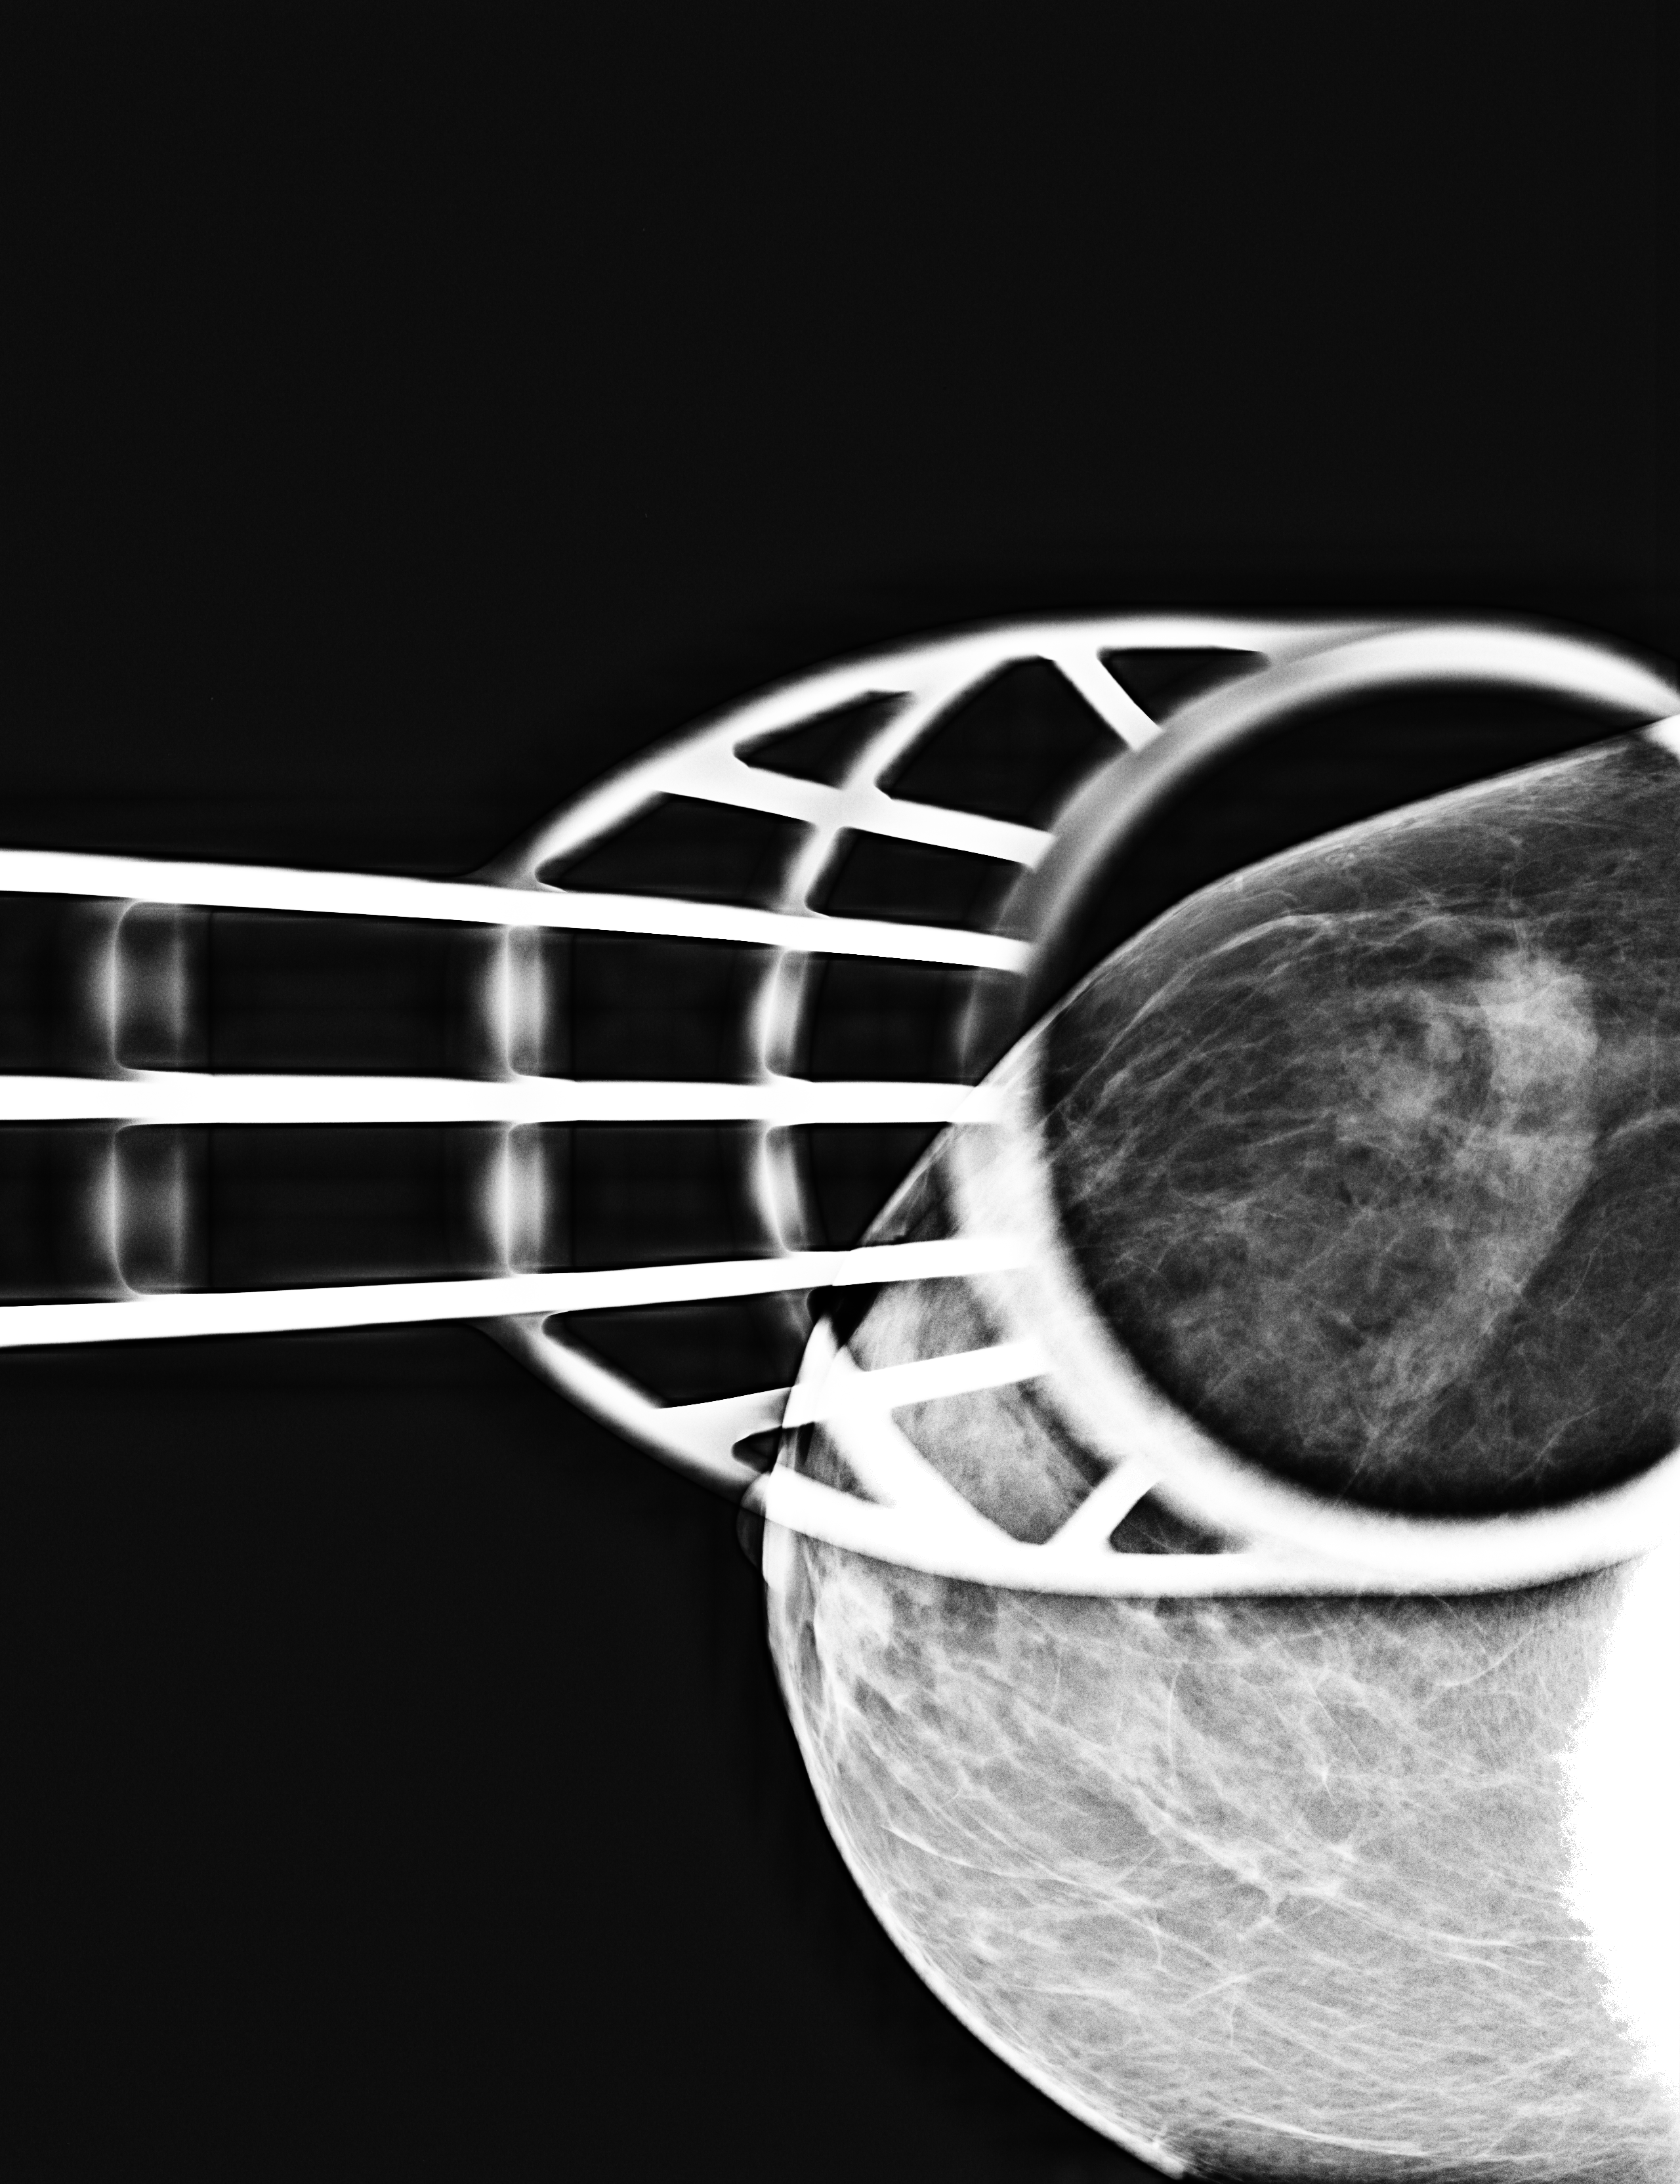
Additional (diagnostic) view; compressed breast thickness 24 mm; system: Selenia Dimensions.
Image type: full-field digital mammogram. Breast: right. Projection: CC view, spot compression.